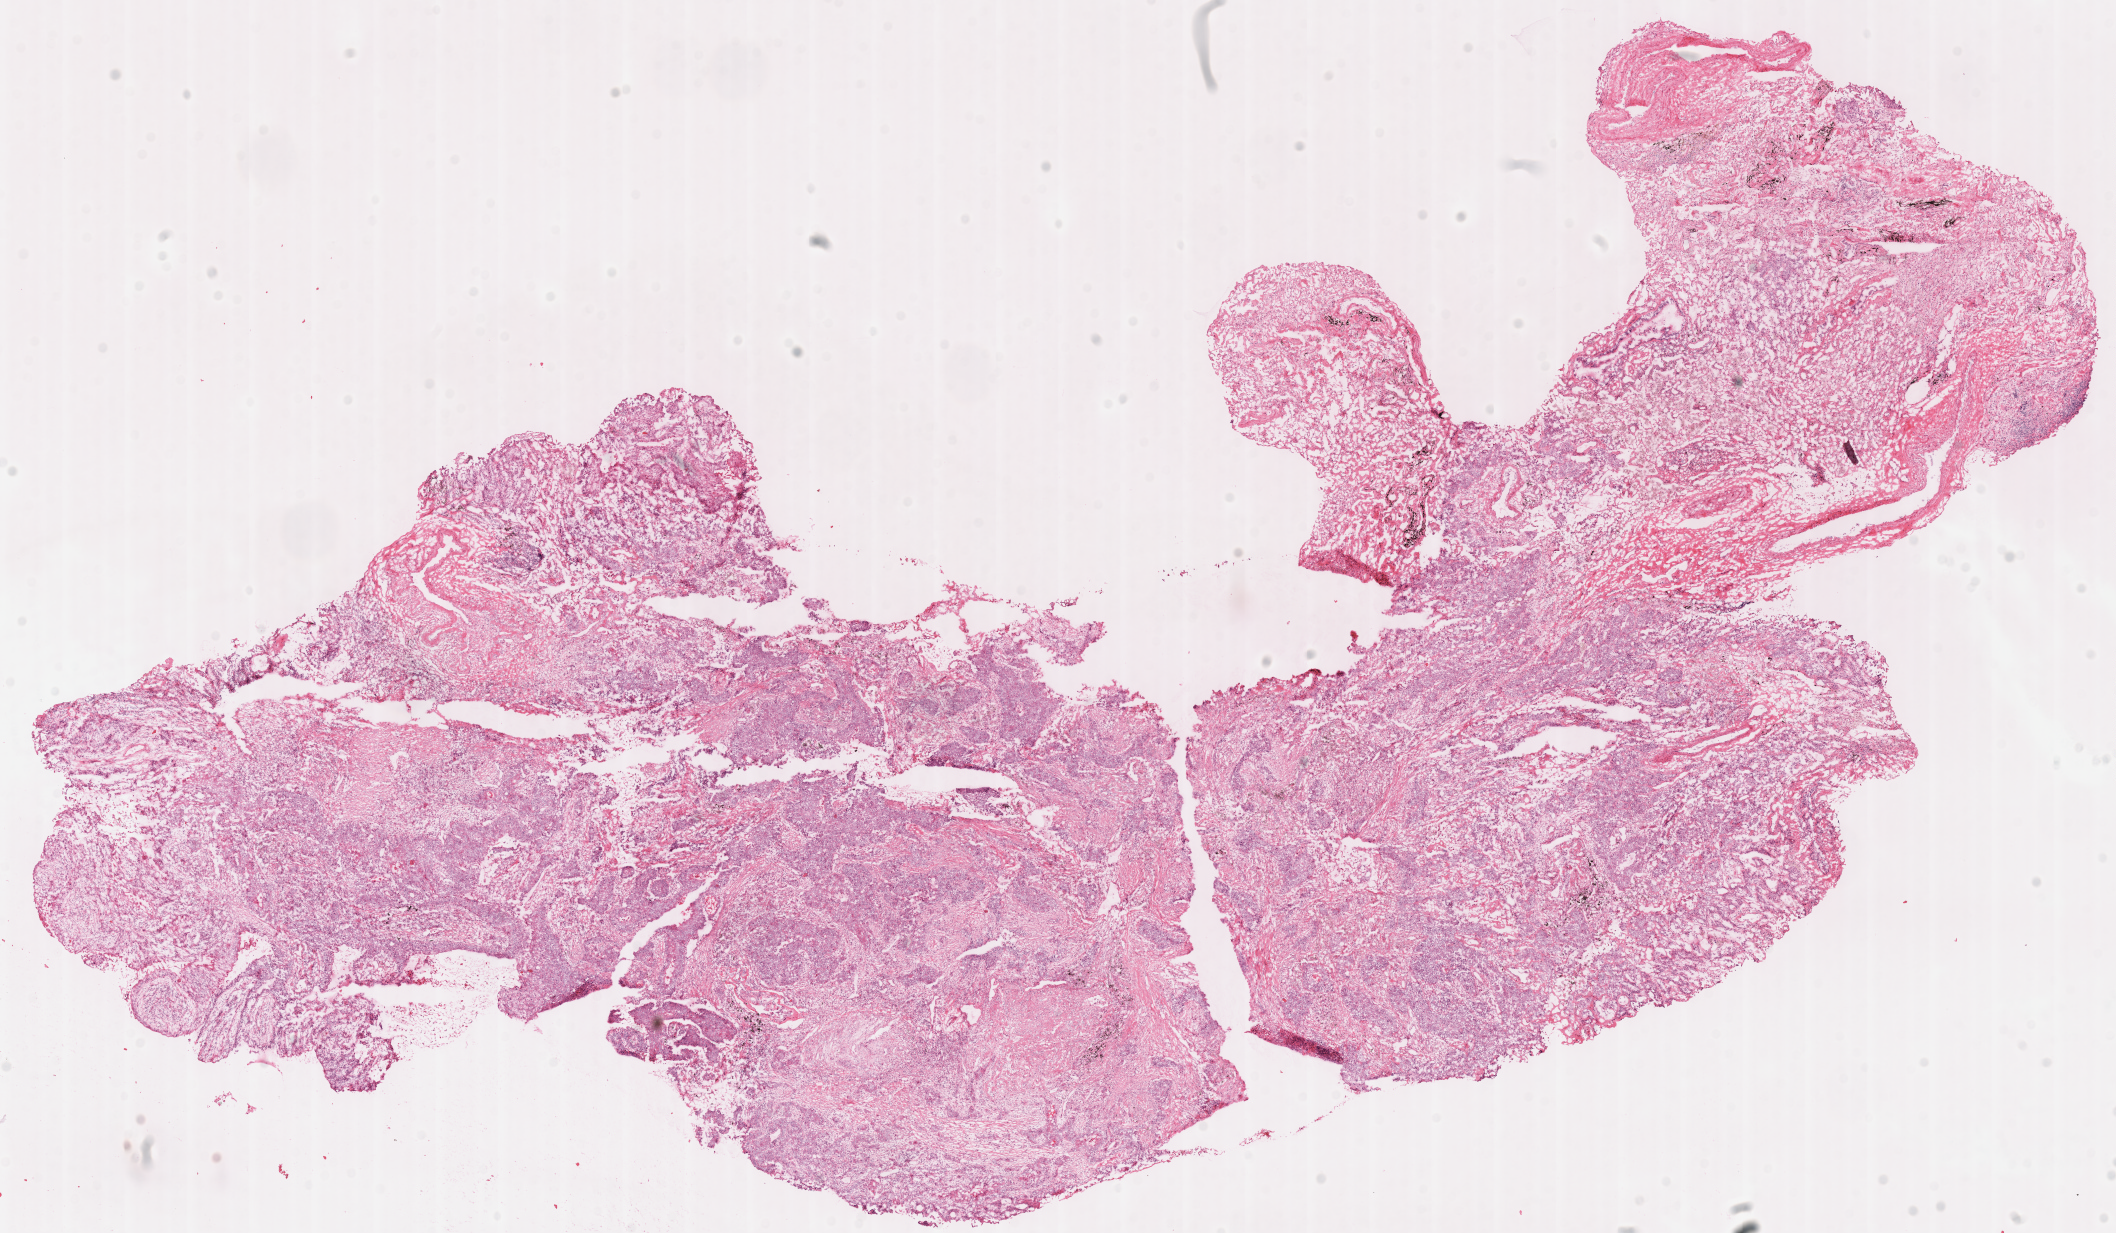
Whole-slide histology image, H&E, low-resolution overview of the scanned area, about 16.6 x 9.7 mm; frozen section from the top of the tissue portion; lung, primary tumour sample. Patient: male, age at initial diagnosis 61 years. Slide review estimates, as recorded: tumour cells 70%, tumour nuclei 70%, normal cells 15%, stromal cells 15%, necrosis 0%.
AJCC pathologic stage: IA (7th edition). Laterality: right. Pathologic diagnosis: Squamous cell carcinoma, NOS (upper lobe, lung).